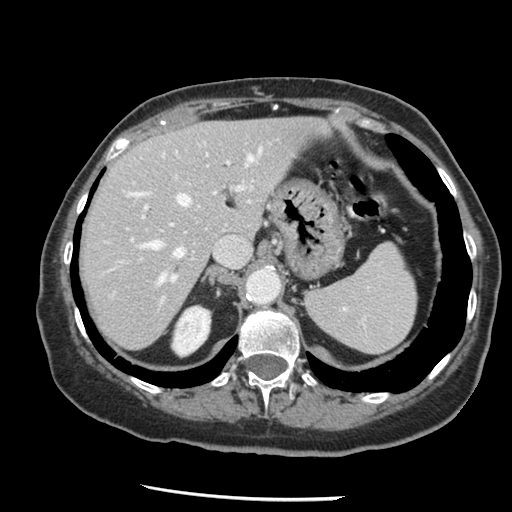
Contrast-enhanced abdominal CT, one axial slice. Slice 98 of 148 in the series (ordered by position). Intravenous contrast given. Soft-tissue window (W 400 / L 40 HU). 512 × 512 image matrix. Female patient, age 85 years. From the clinical record (not read from this slice): diagnosis: colorectal cancer liver metastases, imaged before liver resection; multiple liver metastases: no; largest metastasis: 0.9 cm; disease in both lobes: no.
Annotated regions visible in this slice (outlined manually by an expert reader):
- hepatic veins: bounding box (x1, y1, x2, y2) in pixels: (123, 143, 270, 284)
- liver: (82, 118, 317, 349)
- planned liver remnant (the part of the liver to remain after resection): (82, 118, 317, 349)
- portal vein (with intrahepatic branches): (130, 159, 245, 306)